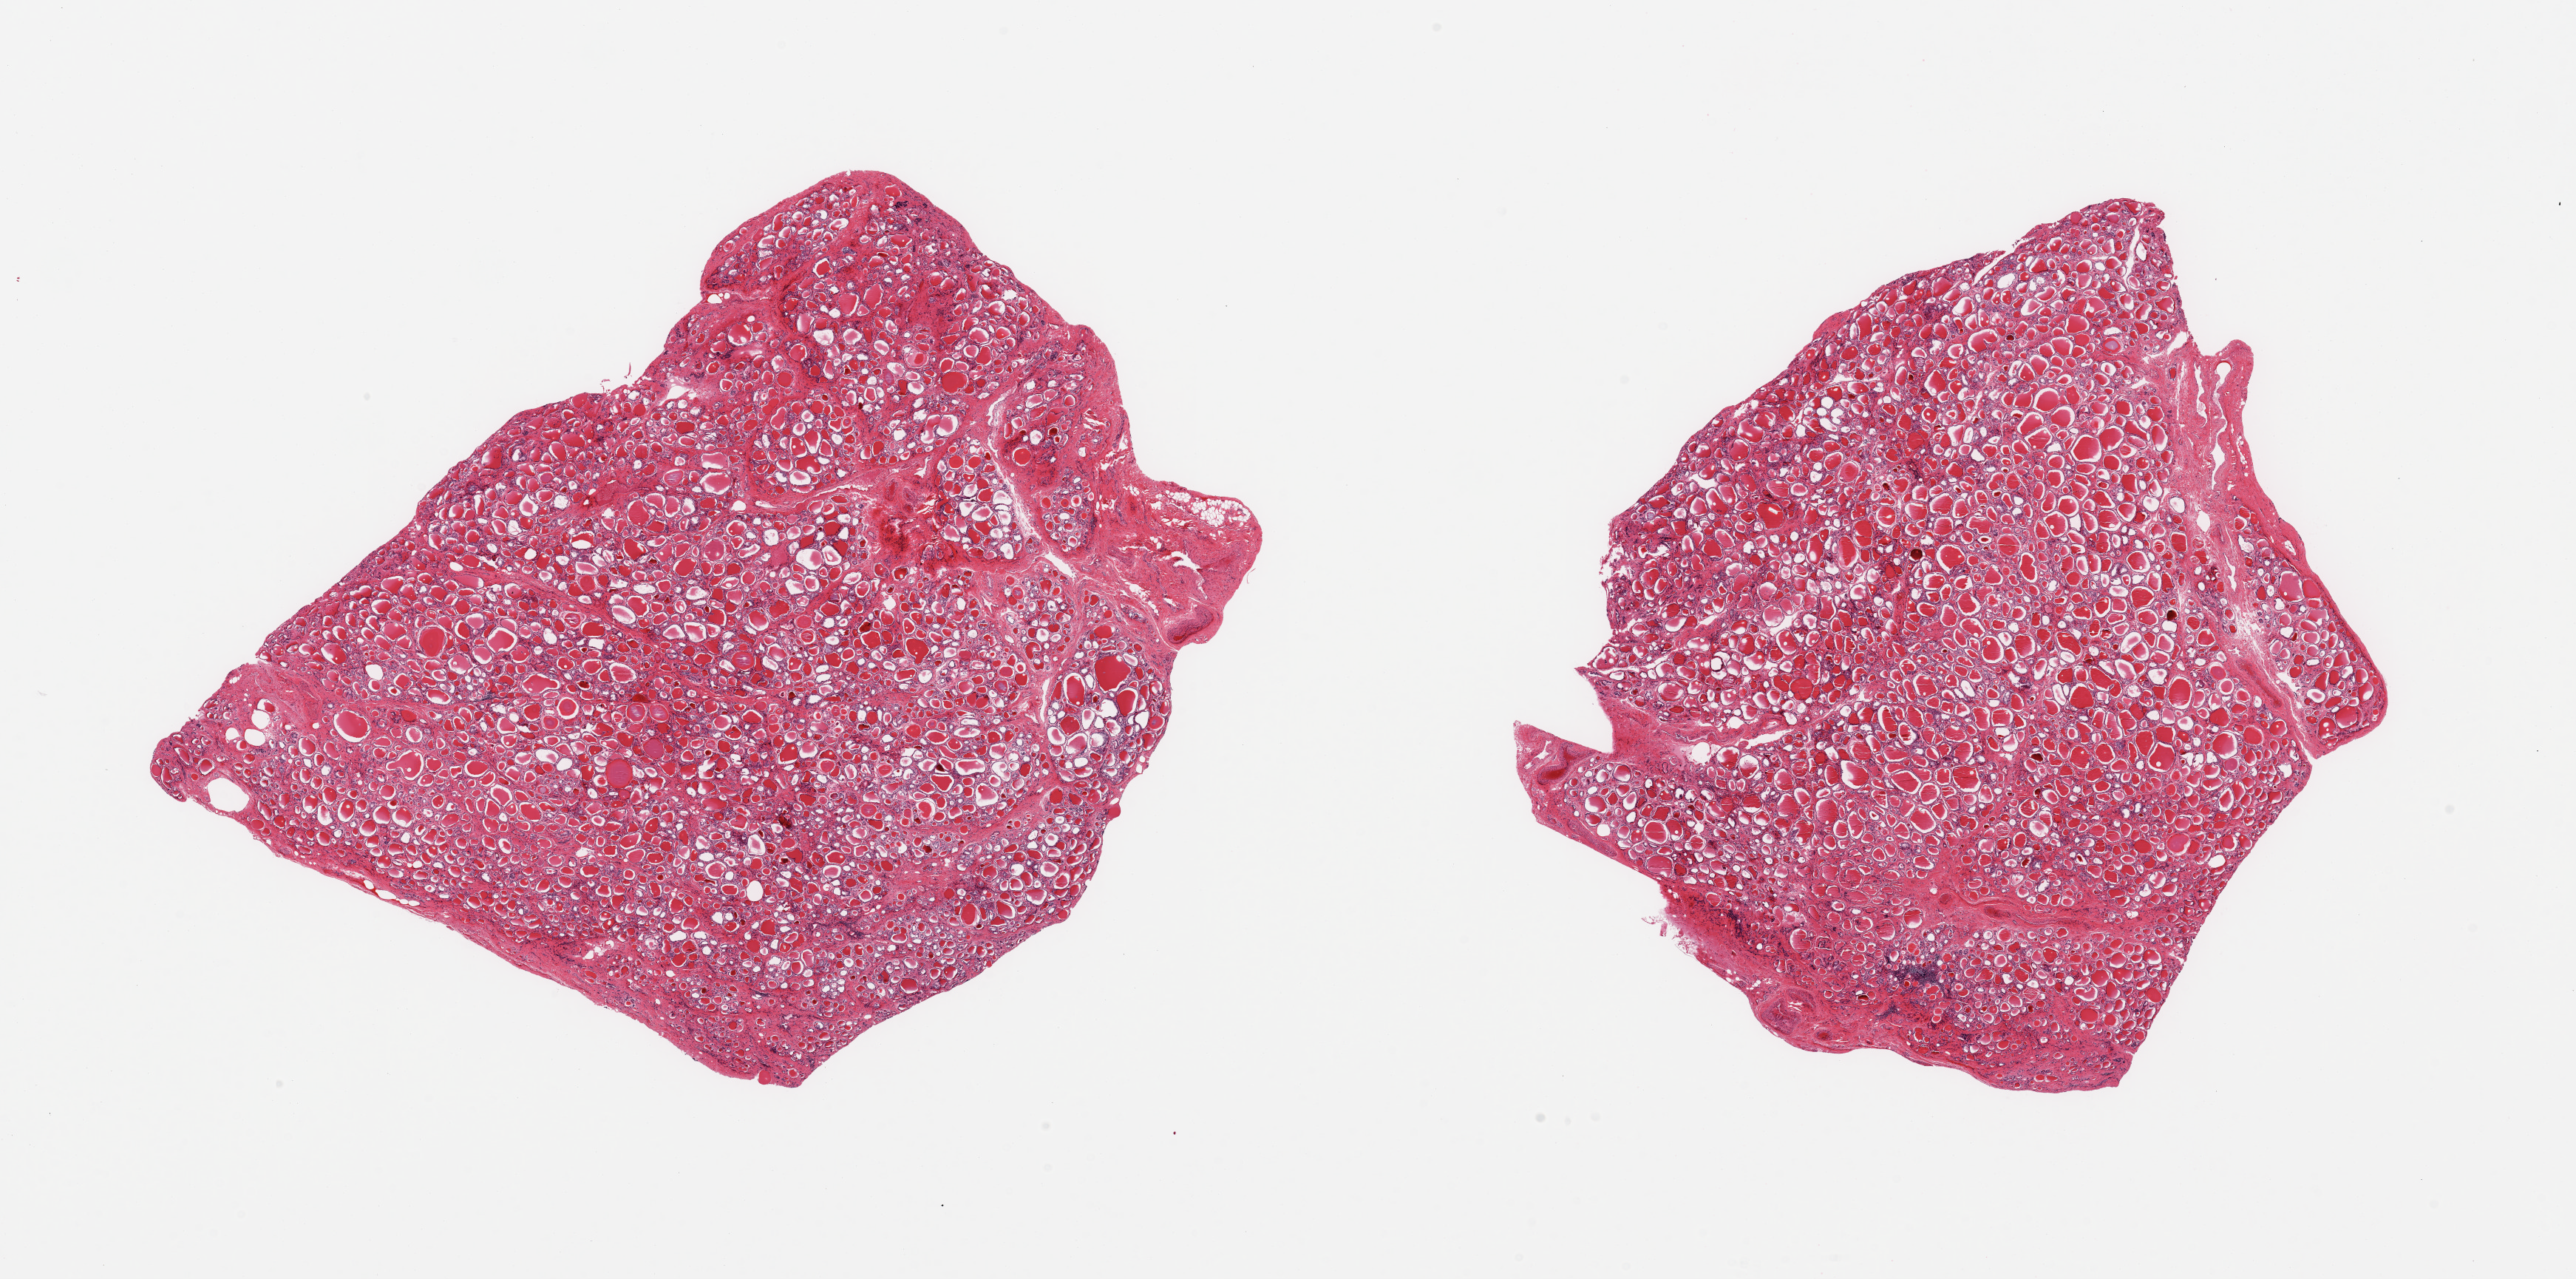
Digitized H&E-stained section, brightfield, shown as a low-resolution overview of the whole scanned area (about 27.6 x 13.7 mm, from a 20x scan), PAXgene-fixed paraffin-embedded (PFPE) section, target tissue: thyroid, tissue donor sample. Donor: male.
Review note (as recorded): 2 pieces; focal interstitial lymphocytic infiltrate.